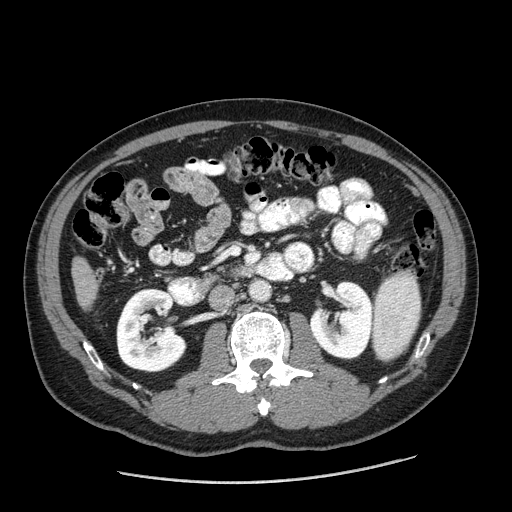
Contrast-enhanced abdominal CT (liver protocol), one axial slice. Slice 49 of 198 in the series (ordered by position). Reconstruction kernel STANDARD. One of 2 acquisitions stored at this slice position. Soft-tissue window (W 400 / L 40 HU). 2.5 mm slice thickness. 512 × 512 image matrix, field of view 400 × 400 mm. From the clinical record (not read from this slice): diagnosis: hepatocellular carcinoma (patient treated with transarterial chemoembolisation; whether this scan precedes or follows treatment is not stated here); TNM stage (as recorded): Stage-II; Child-Pugh class: A; tumour differentiation: moderately differentiated; tumour nodularity: multinodular.
Outlined on this slice (semi-automatic segmentation, software-assisted and operator-edited):
- liver parenchyma outside the tumour (the mass and vessels are separate outlines, so this box may not span the whole liver): bounding box (x1, y1, x2, y2) in pixels: (72, 258, 96, 308)